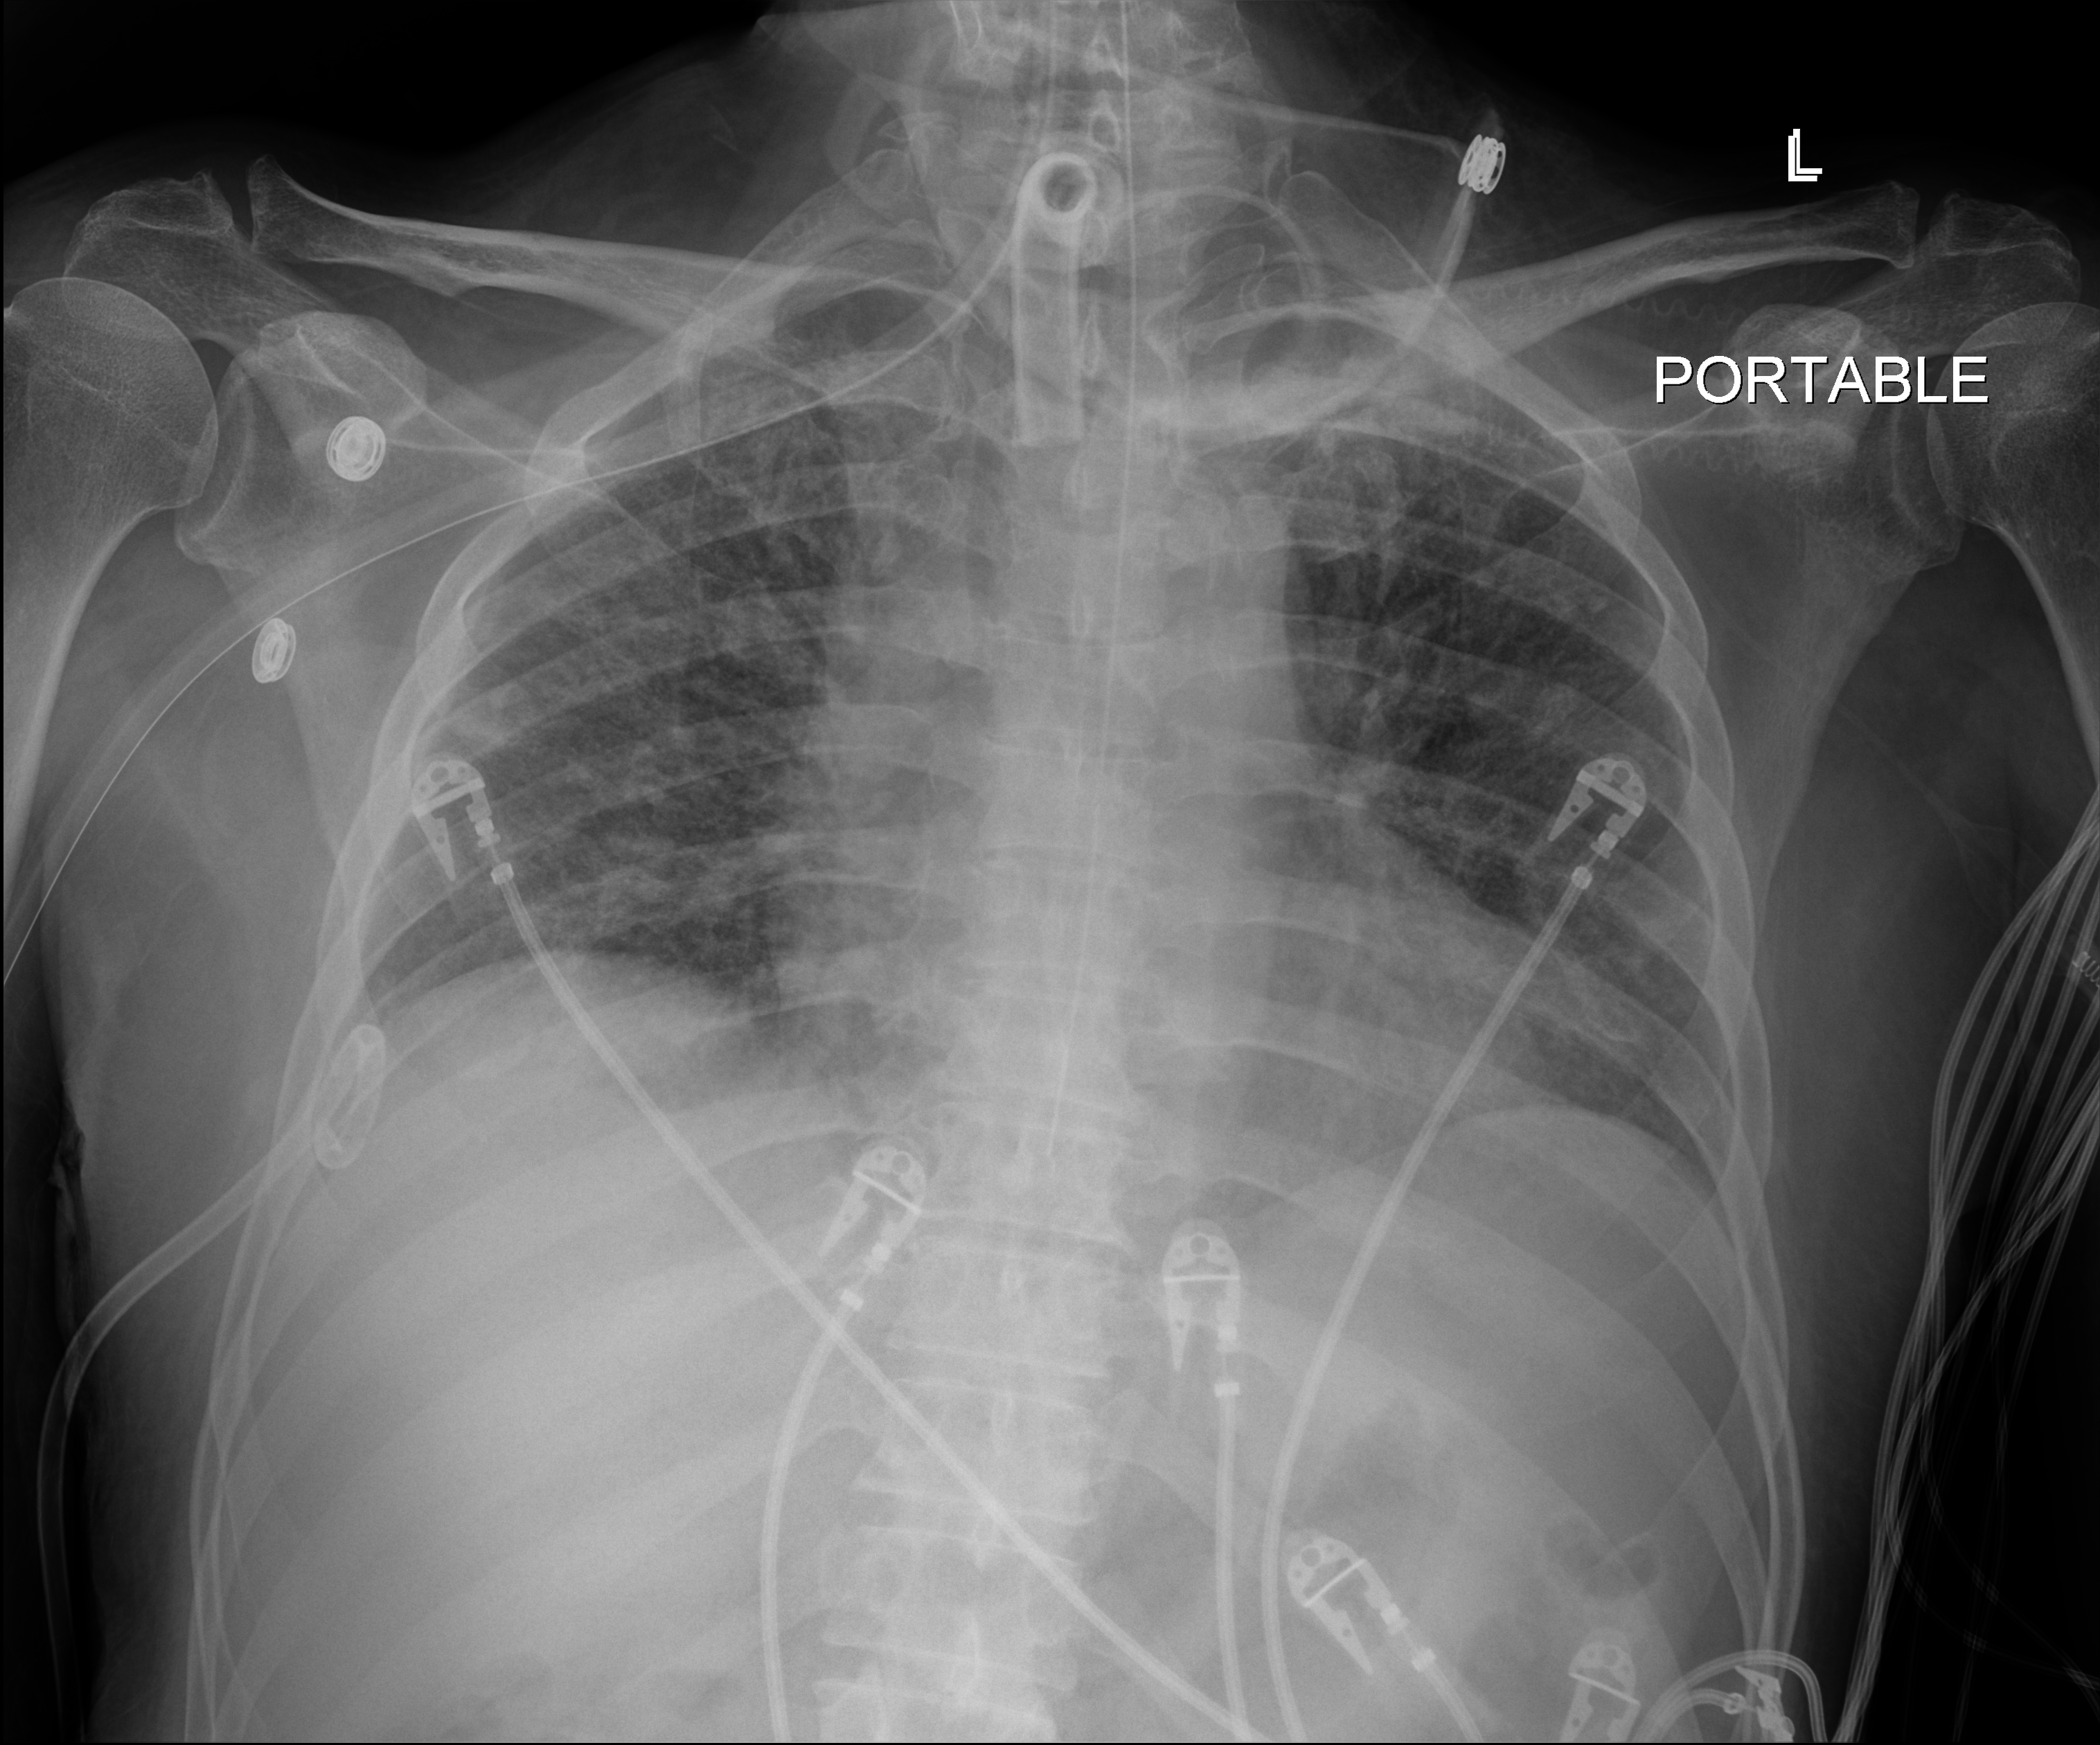
Bedside chest radiograph (digital radiography); anteroposterior (AP) projection. Male patient hospitalised with COVID-19, age 18–59 years.
Admission-level facts for this patient (not findings on this image; timing relative to this image not recorded): diabetes (admission record): no; admitted to intensive care during this hospital stay: yes; chronic kidney disease (admission record): no.